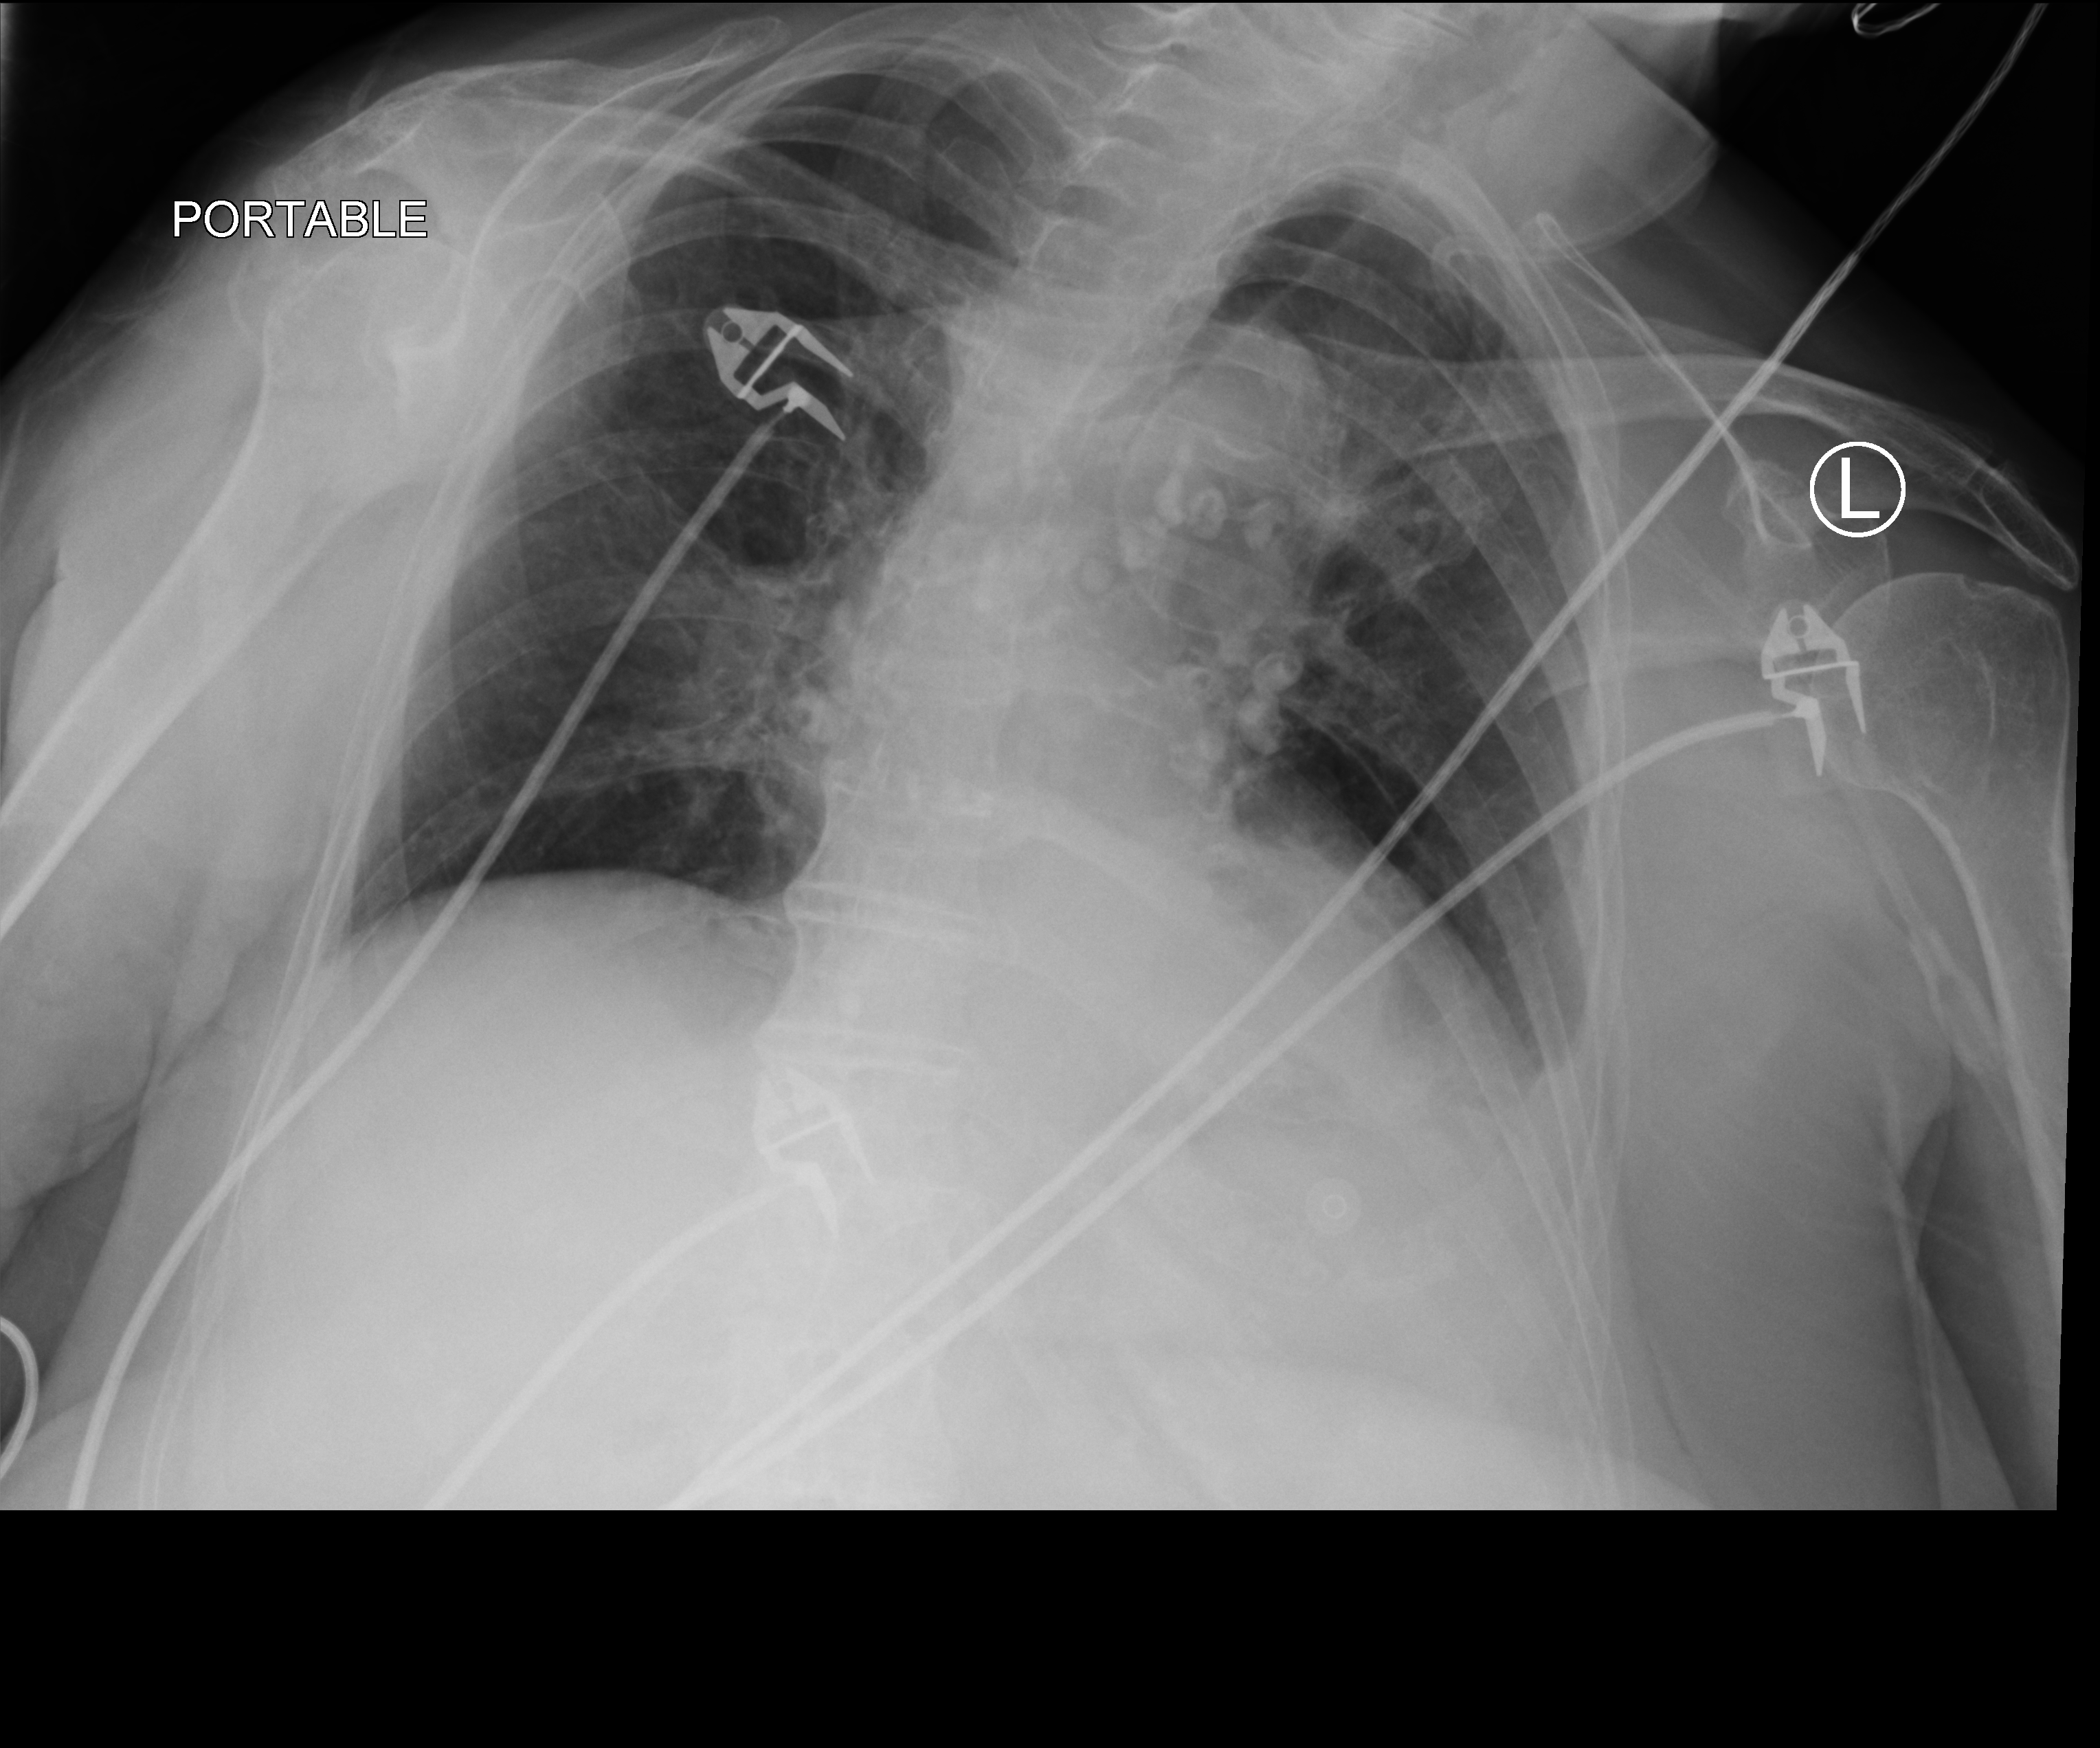
Portable chest radiograph, anteroposterior (AP) projection. Patient hospitalised with COVID-19; female, aged 75–90 years.
Admission-level facts for this patient (not findings on this image; timing relative to this image not recorded): mechanically ventilated during this hospital stay: no.